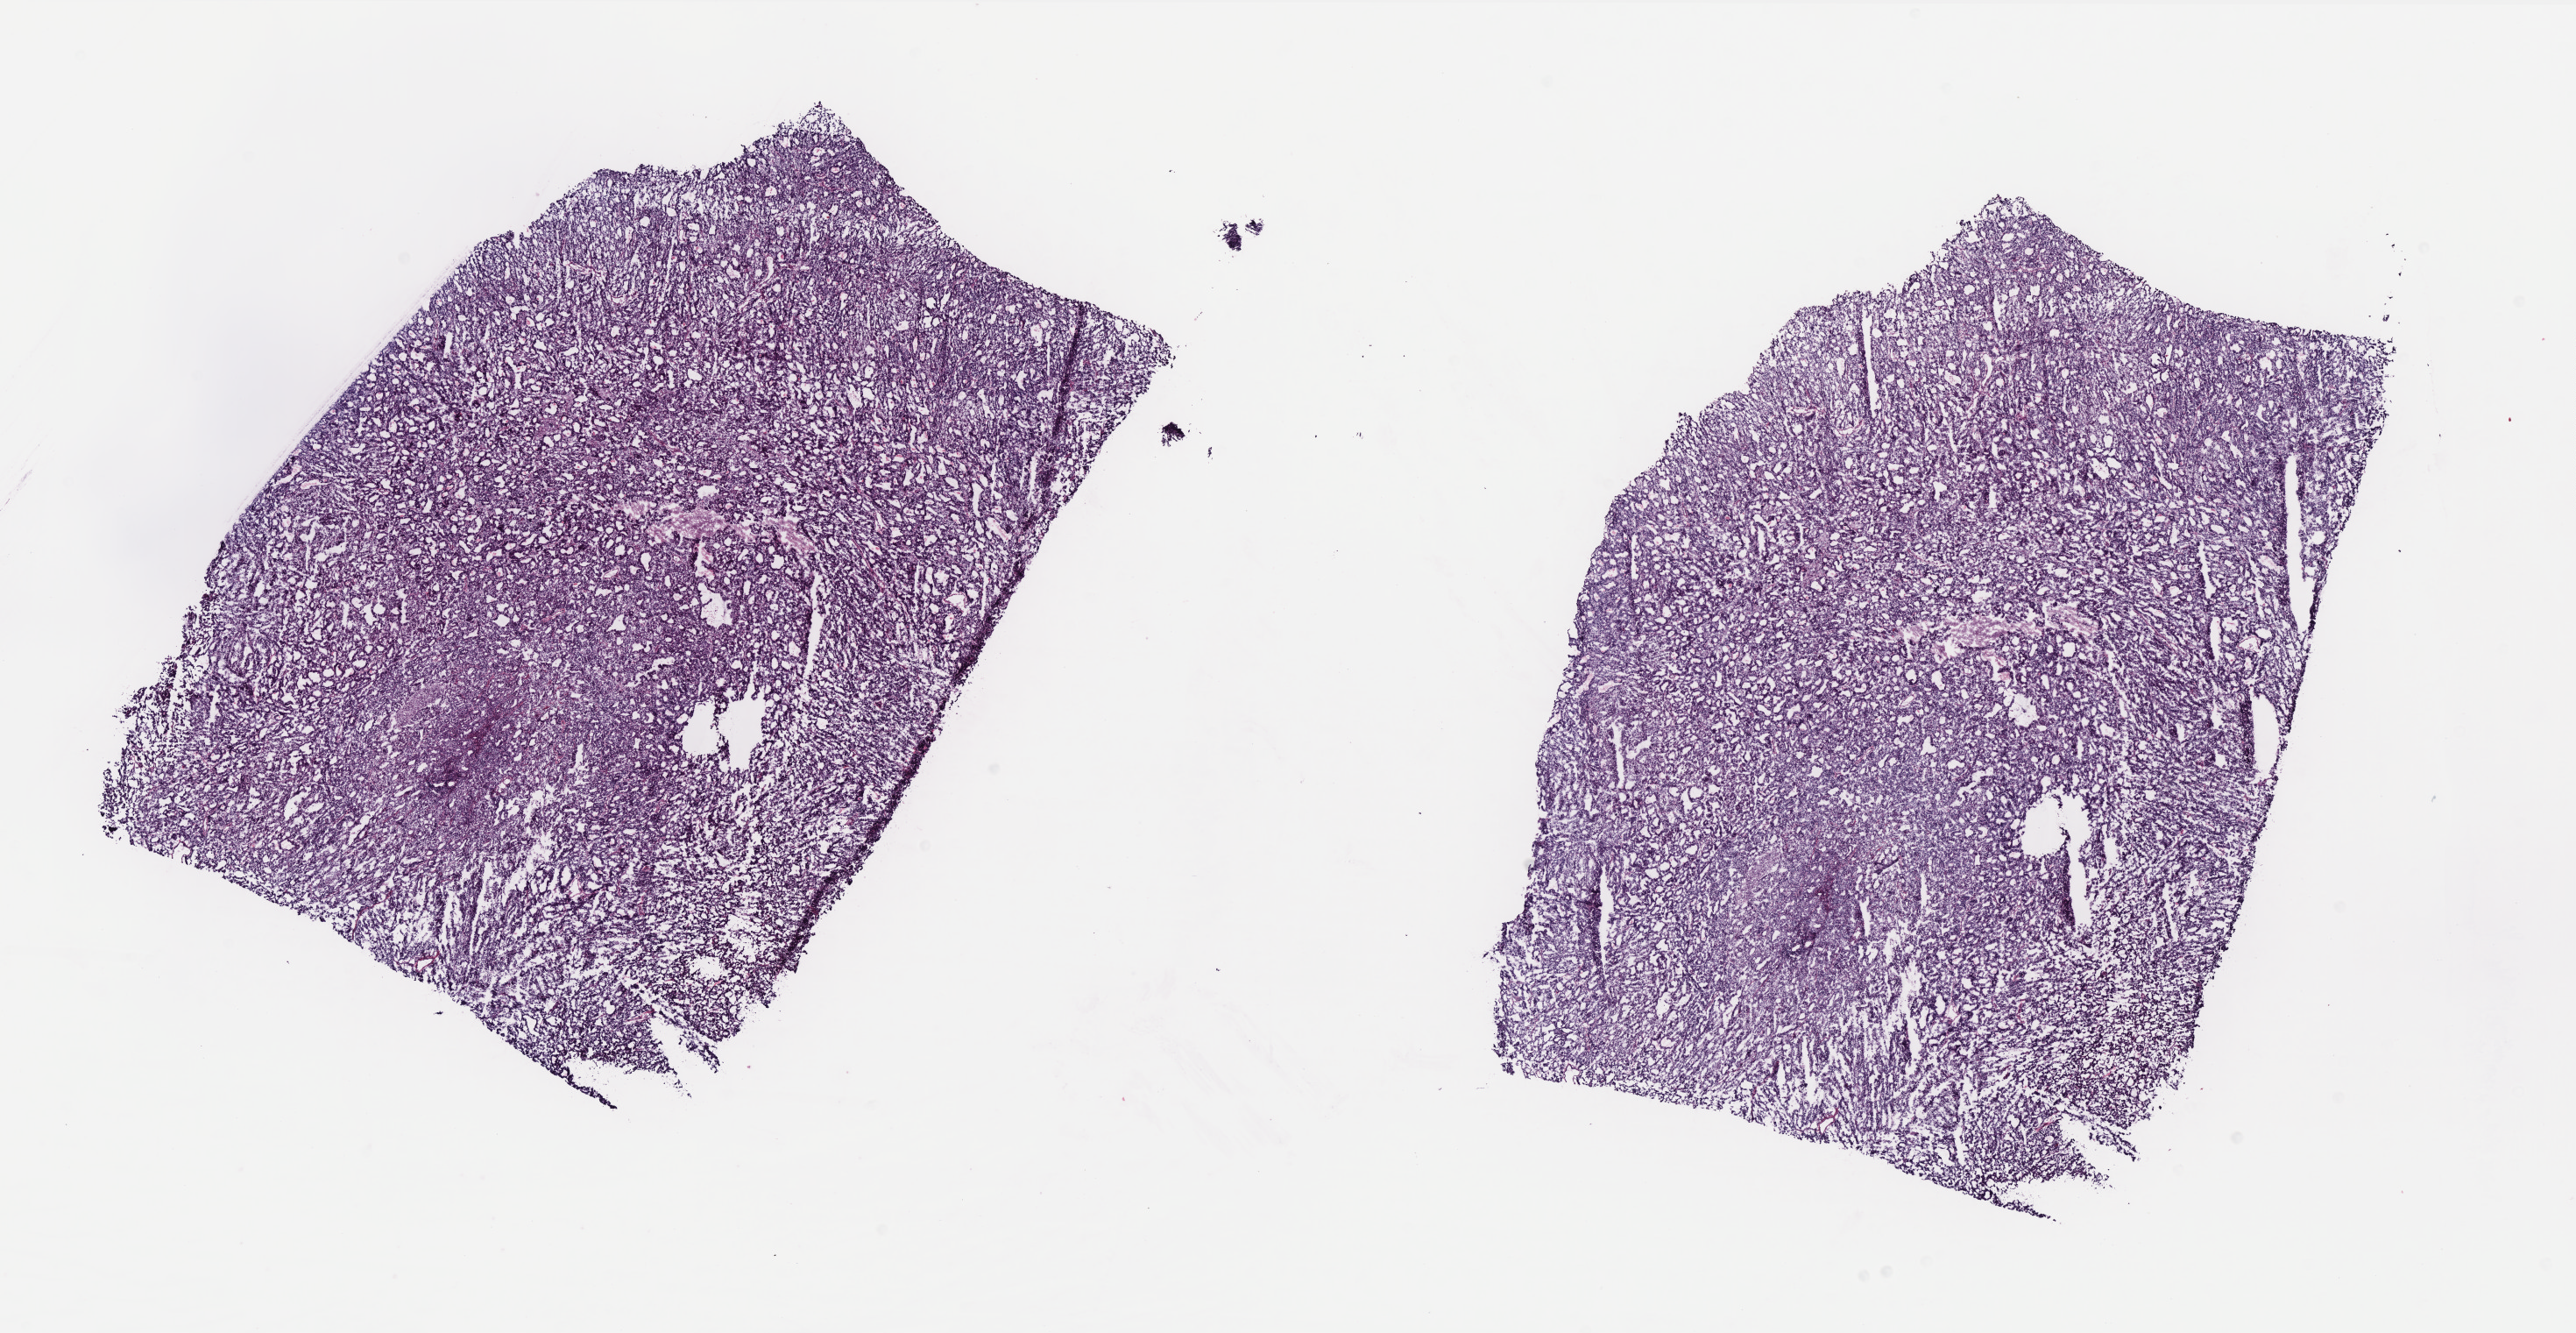
Whole-slide histology image, H&E, whole scanned area (about 23.6 x 12.2 mm) shown as a low-resolution overview; frozen section from the top of the tissue portion; primary tumour sample from the uterus. Female patient; age at initial diagnosis 74 years. Histologic grade: G2 (moderately differentiated). Composition of this section per pathologist review: tumour cells 95%, tumour nuclei 90%, normal cells 0%, stromal cells 0%, necrosis 5%. Infiltration values recorded for this section: lymphocyte infiltration 0%, monocyte infiltration 0%, neutrophil infiltration 0%.
FIGO stage: IB. Lymph nodes positive (case pathology): 0 of 12 examined. Diagnosis: Endometrioid adenocarcinoma, NOS (endometrium).